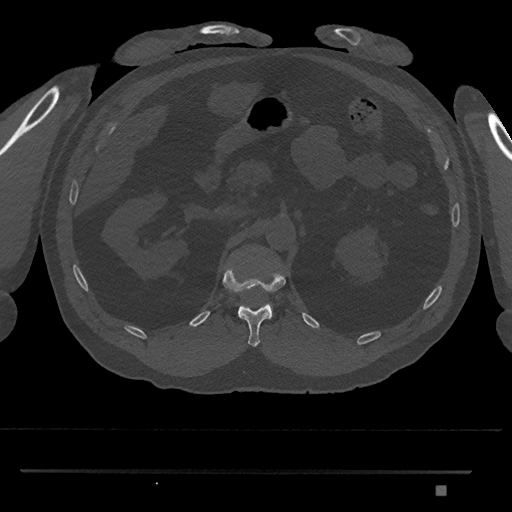
CT including the spine, one axial slice. 120 kVp. Bone window (W 1800 / L 400 HU). 512 × 512 image matrix, field of view 429 × 429 mm. Male patient, age 65 years. From the clinical record (not read from this slice): primary cancer: prostate.
Outlined on this slice (semi-automatic segmentation, software-assisted and operator-edited):
- L1 vertebra: bounding box (x1, y1, x2, y2) in pixels: (270, 305, 273, 318)
- T12 vertebra: (223, 265, 286, 347)